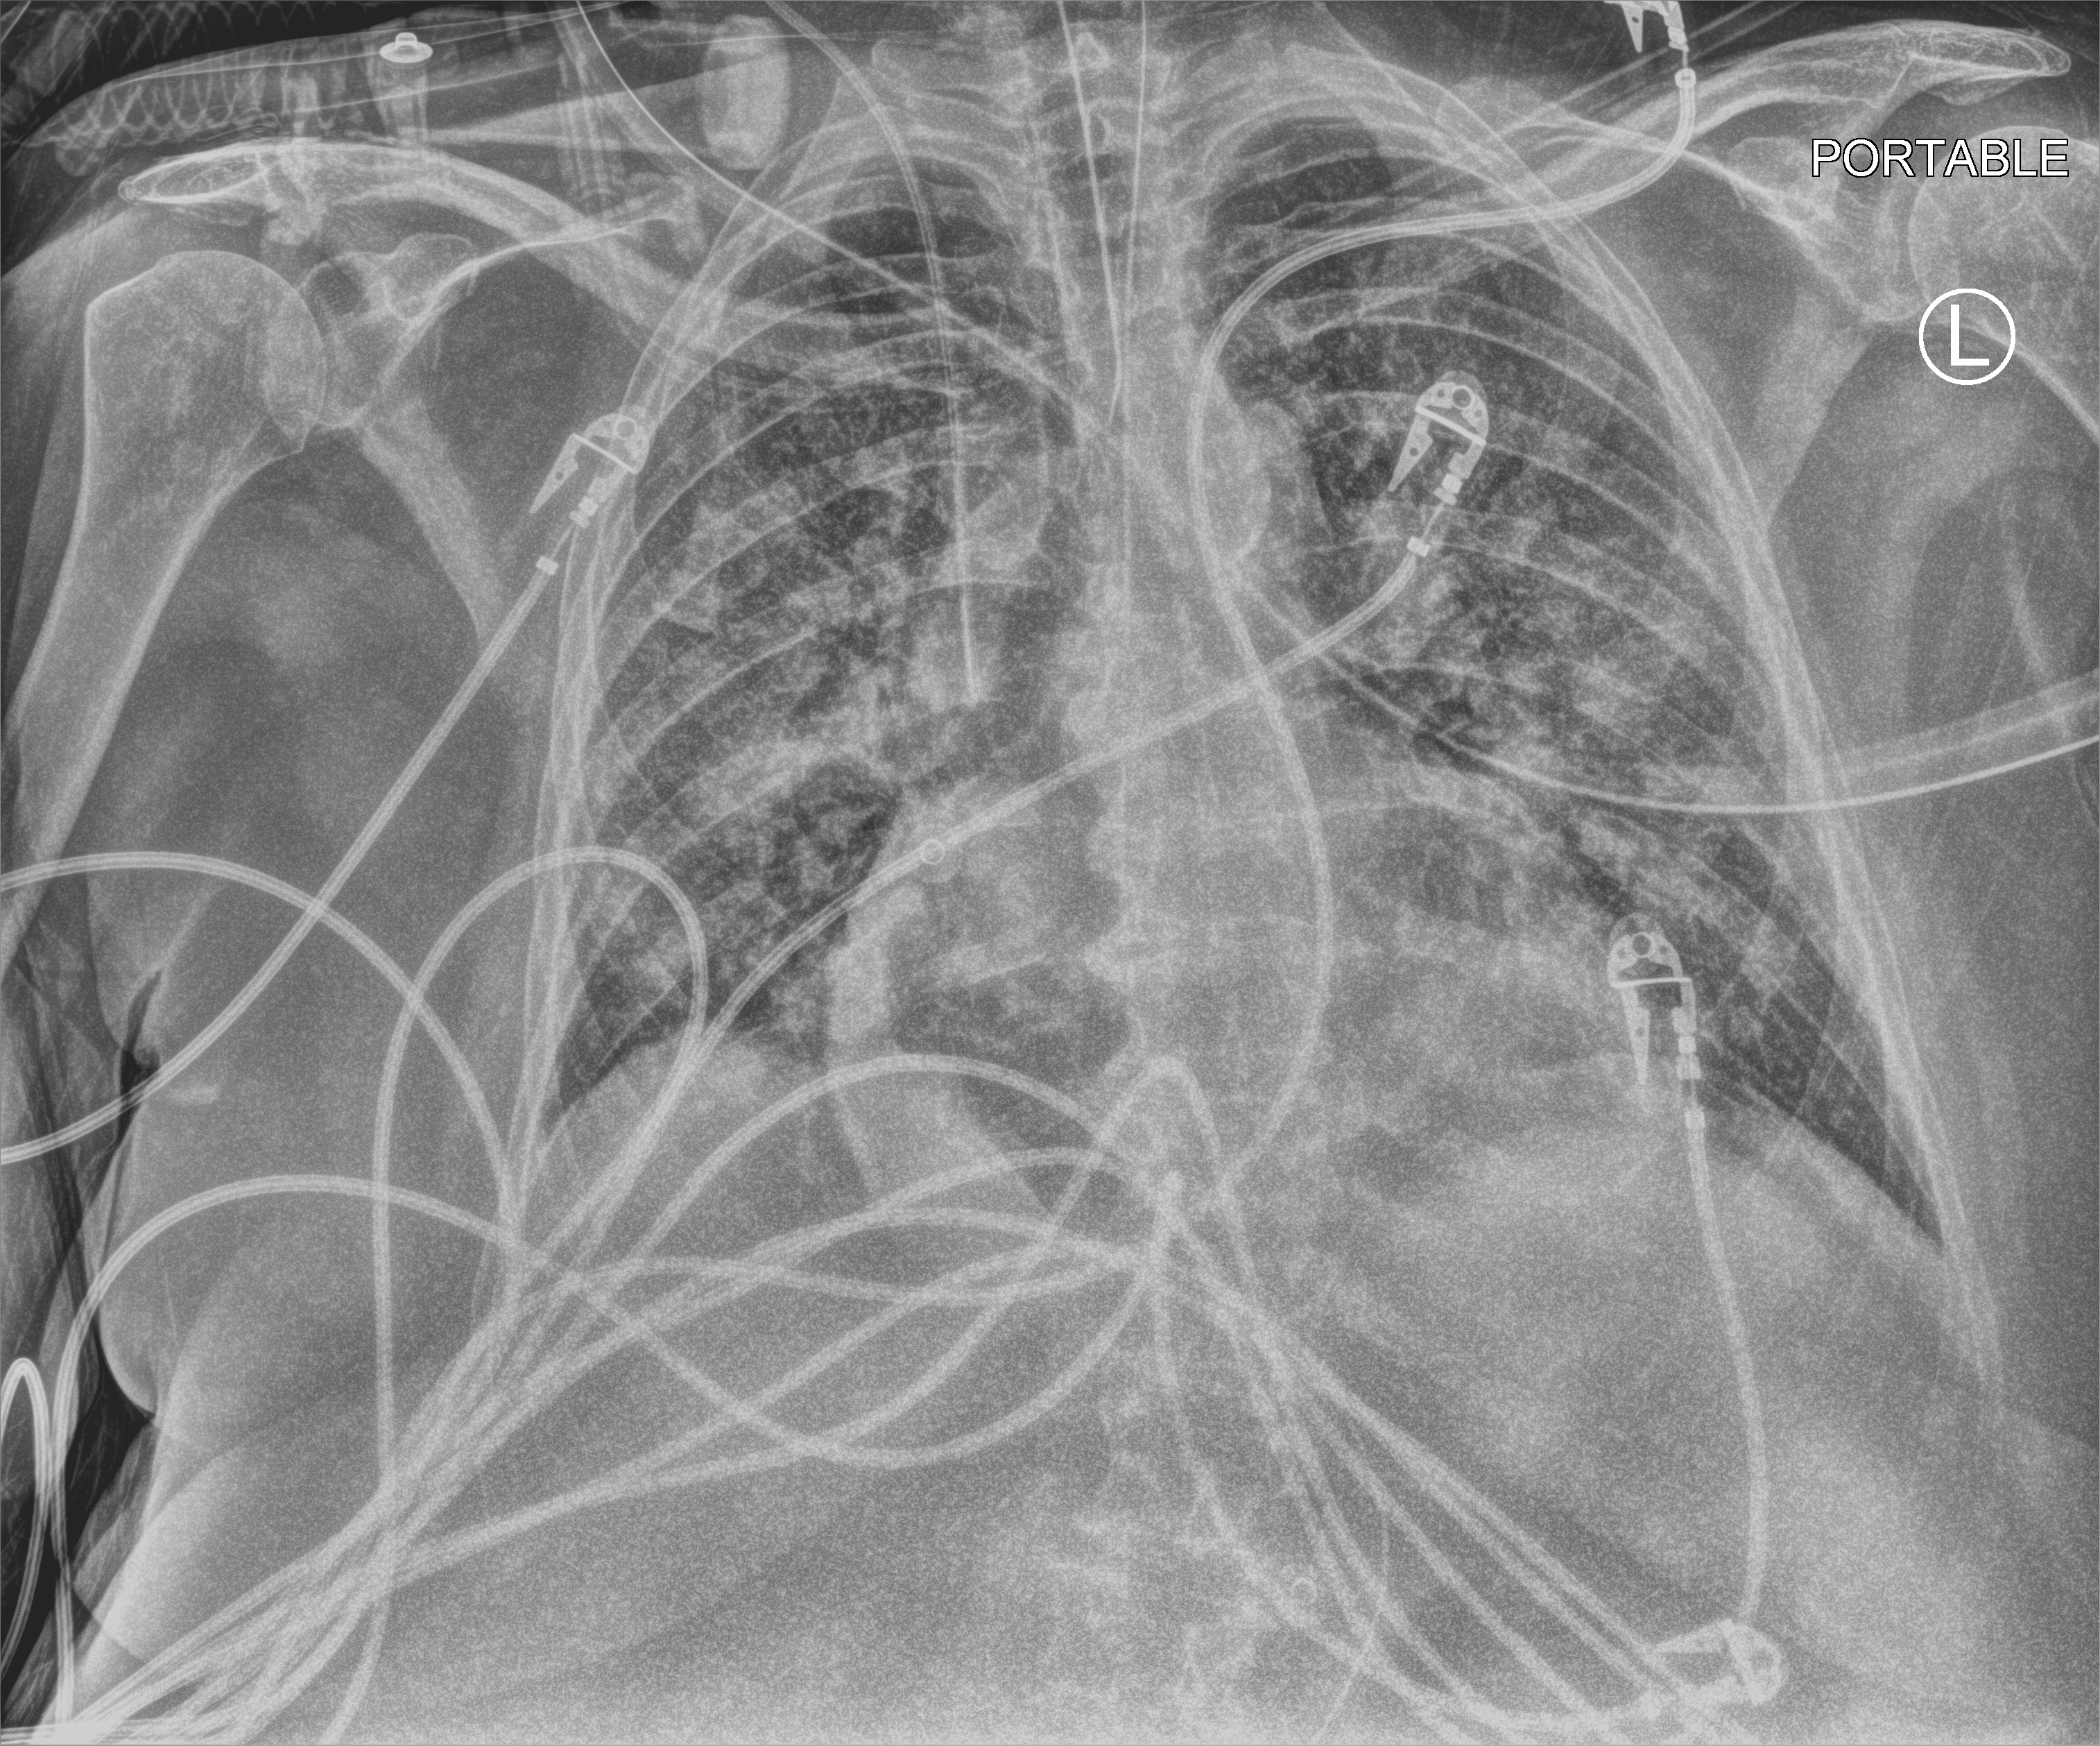
Bedside chest radiograph (computed radiography); anteroposterior (AP) projection. Female patient hospitalised with COVID-19, age 75–90 years.
Admission-level facts for this patient (not findings on this image; timing relative to this image not recorded): mechanically ventilated during this hospital stay: yes; length of hospital stay: 31 days.